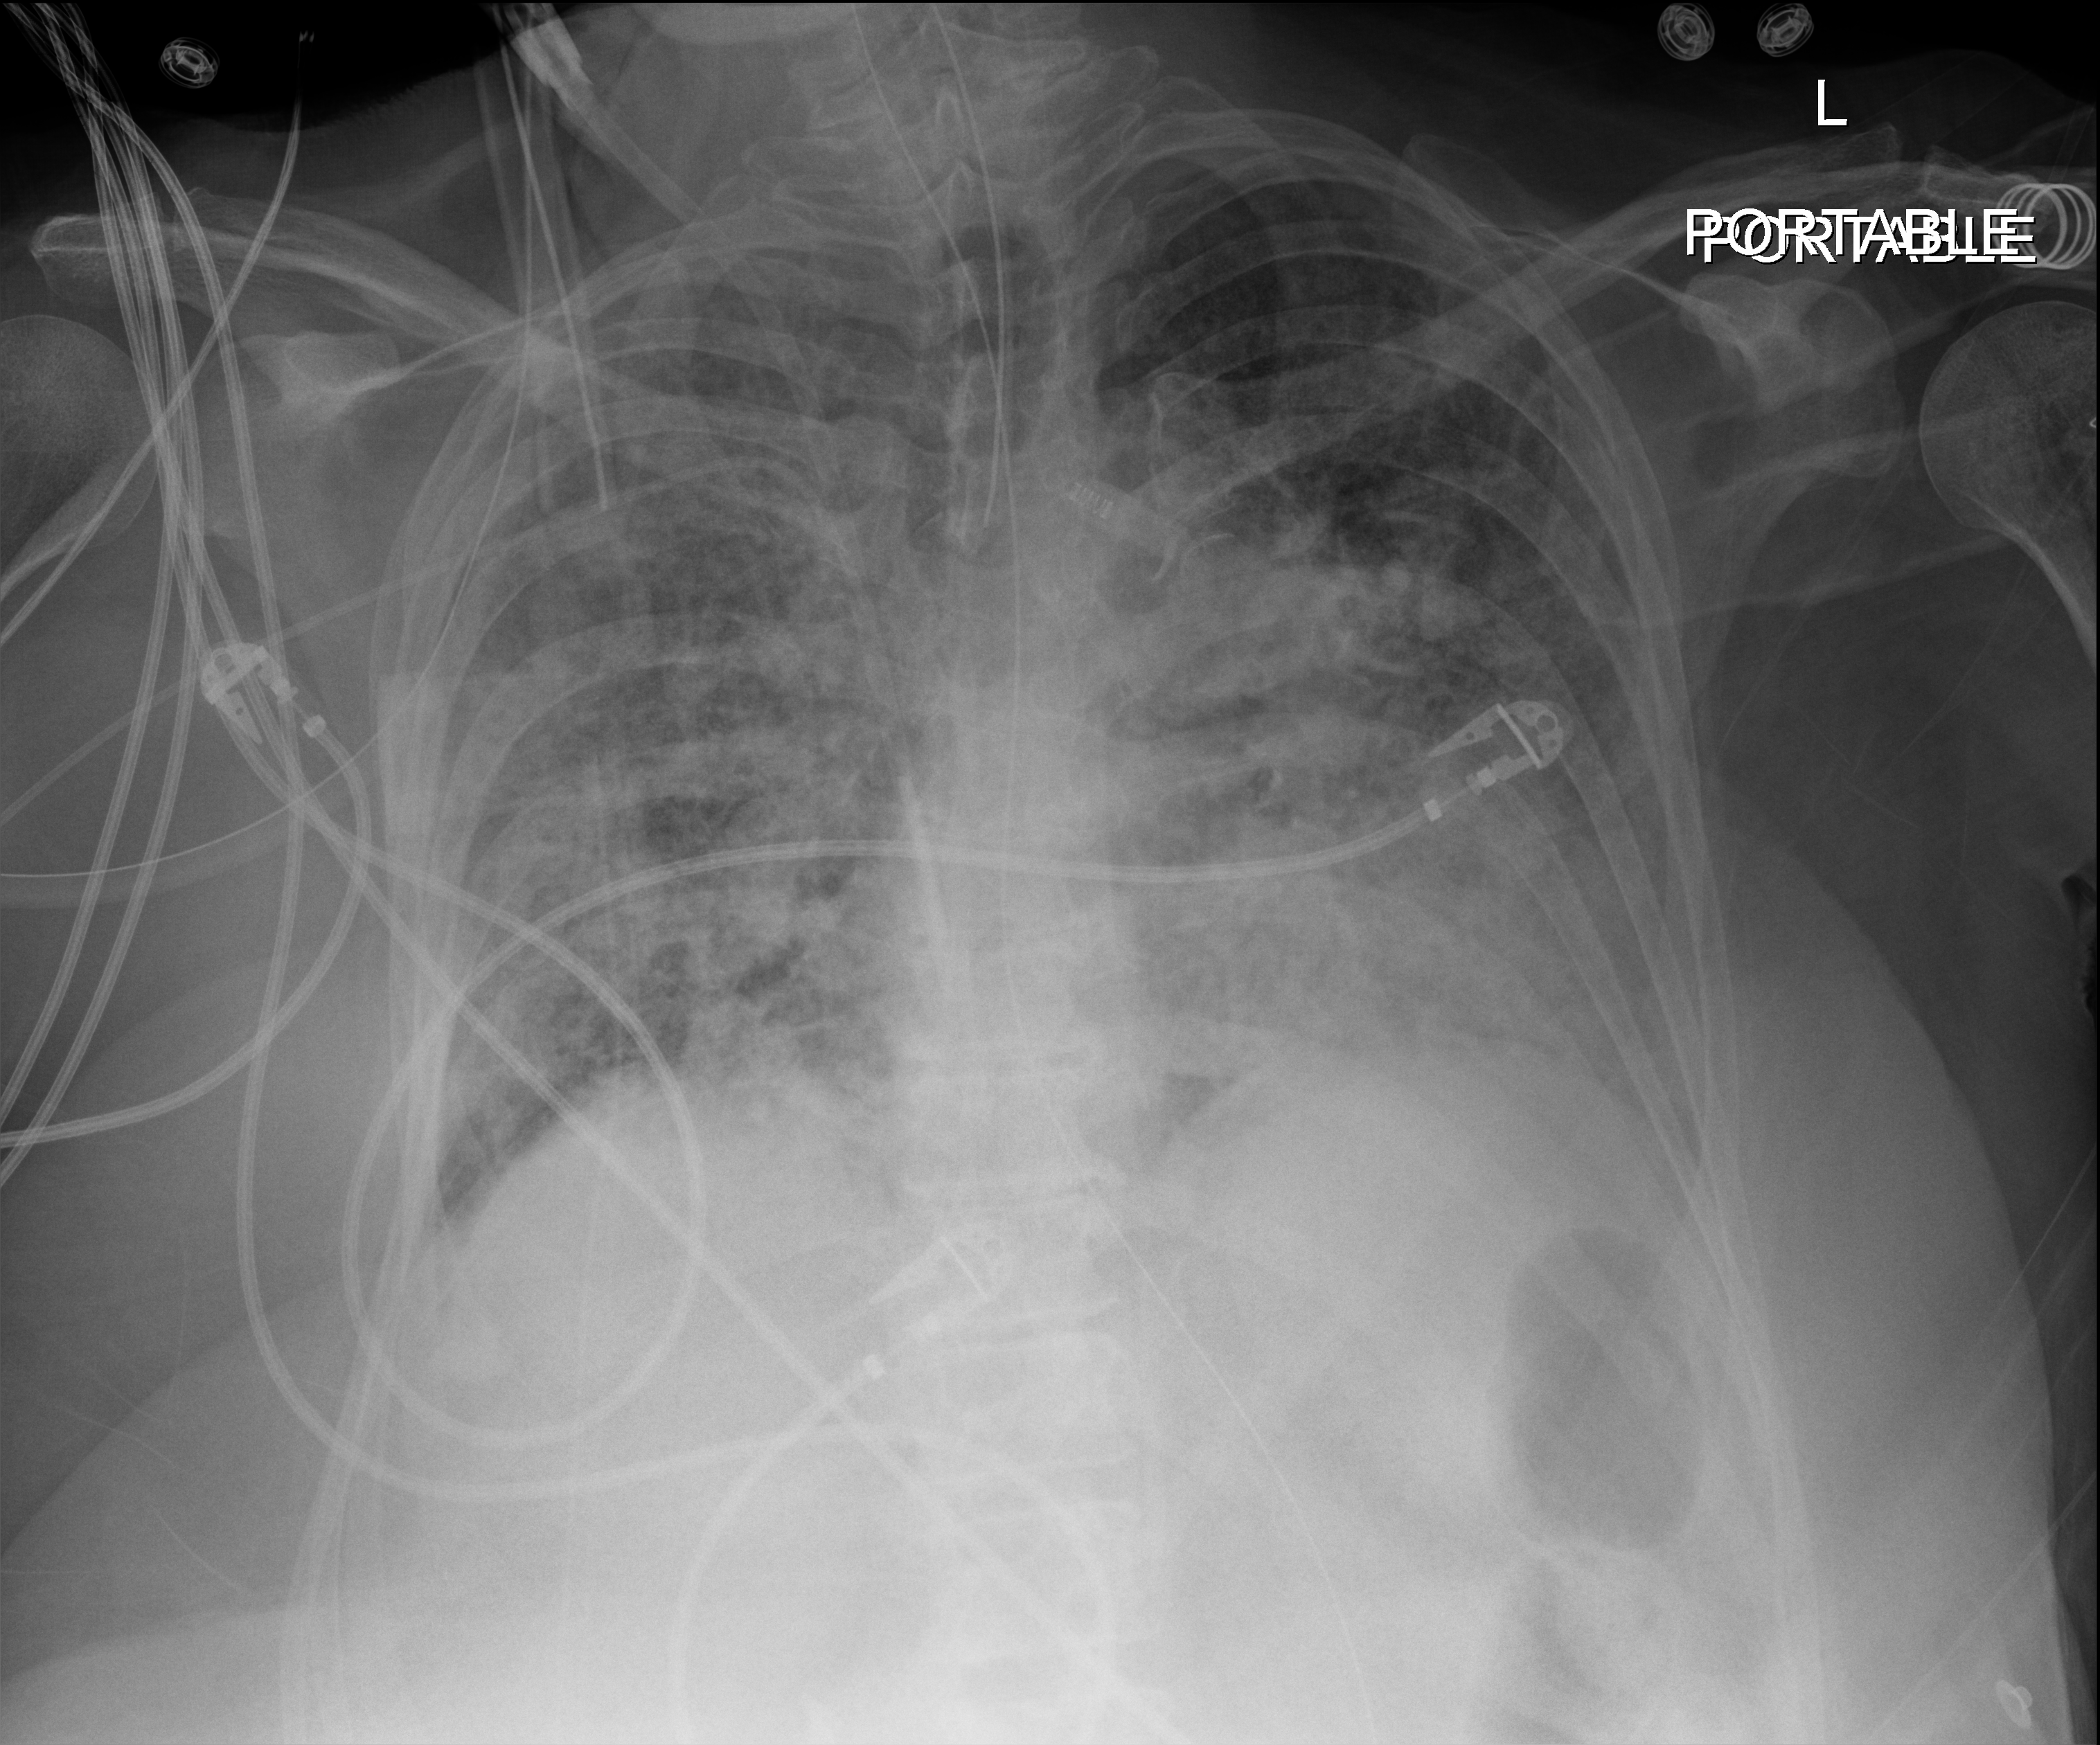
Chest X-ray (portable), anteroposterior (AP) projection. Female patient hospitalised with COVID-19, age 60–74 years.
Hospital-stay facts (about this admission, not read from this image; timing relative to this image not recorded):
- mechanically ventilated during this hospital stay: yes
- admitted to intensive care during this hospital stay: yes
- COPD (admission record): no